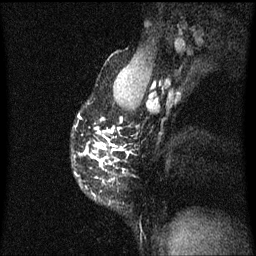
Breast MRI (dynamic contrast-enhanced), one sagittal slice; slice 44 of 60 in the series (ordered by position); dynamic contrast-enhanced series, image 2 of 3 at this slice position (ordered by acquisition); 1.5 T; TE 4.2 ms, TR 8.4 ms; 2 mm slice thickness; 256 × 256 image matrix, field of view 200 × 200 mm. Female patient, age 40 years.
Annotated regions visible in this slice (semi-automatically segmented with operator editing):
- analysis volume of interest (the breast-tissue region the enhancement analysis was run in; not a lesion): bounding box <76,114,124,201> (left, top, right, bottom; pixels)
- tumour enhancement mask (voxels above the 70 % enhancement threshold inside the analysis volume of interest): <79,116,122,171>